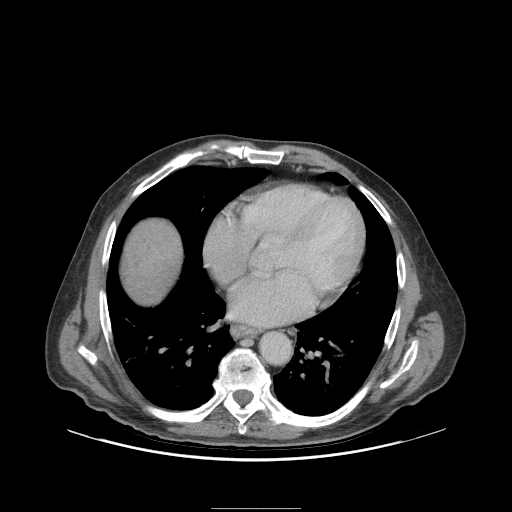
Contrast-enhanced abdominal CT (liver protocol), one axial slice. Position 98 of 105 along the scan axis. Reconstruction kernel STANDARD. 140 kVp. Soft-tissue window (W 400 / L 40 HU). 2.5 mm slice thickness. 512 × 512 image matrix, field of view 440 × 440 mm. Case-level facts recorded for this patient, not image findings: diagnosis: hepatocellular carcinoma (patient treated with transarterial chemoembolisation; whether this scan precedes or follows treatment is not stated here); TNM stage (as recorded): Stage-I; Child-Pugh class: A; tumour nodularity: uninodular; tumour size: 5.1 cm.
Outlined on this slice (semi-automatic segmentation, software-assisted and operator-edited):
- liver parenchyma outside the tumour (the mass and vessels are separate outlines, so this box may not span the whole liver): bounding box (x1, y1, x2, y2) in pixels: (120, 218, 182, 304)